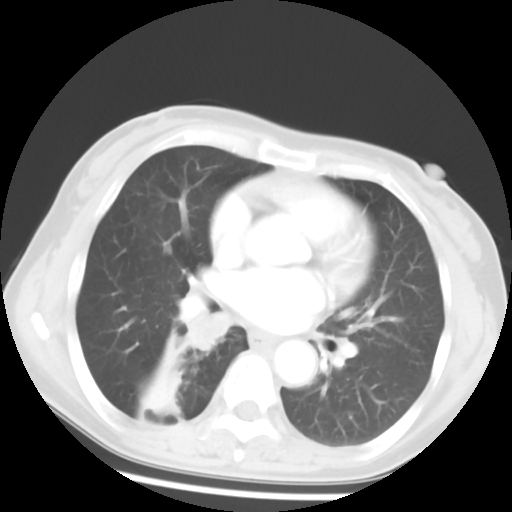
Chest CT, one axial slice; reconstruction kernel STANDARD; lung window (W 1500 / L -600 HU); 5 mm slice thickness; 512 × 512 image matrix, field of view 297 × 297 mm. Female patient, age 54 years. From the clinical record (not read from this slice): clinical TNM (as recorded): T1c N0 M0.
Annotated regions visible in this slice (rectangle marked by the reading radiologist):
- lung tumour (recorded histology: squamous cell carcinoma): bounding box <178,300,237,361> (left, top, right, bottom; pixels)